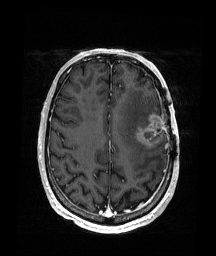
Brain MRI from a brain-tumour surgery series, one axial slice; T1-weighted post-contrast; 1 mm slice thickness; 216 × 256 image matrix, field of view 219 × 260 mm. From the clinical record (not read from this slice): histopathology: Glioblastoma; WHO grade: 4; IDH mutation: no.
Structures marked on this image (outlined manually by an expert reader):
- tumour: bounding box (x1, y1, x2, y2) in pixels: (135, 112, 168, 148)